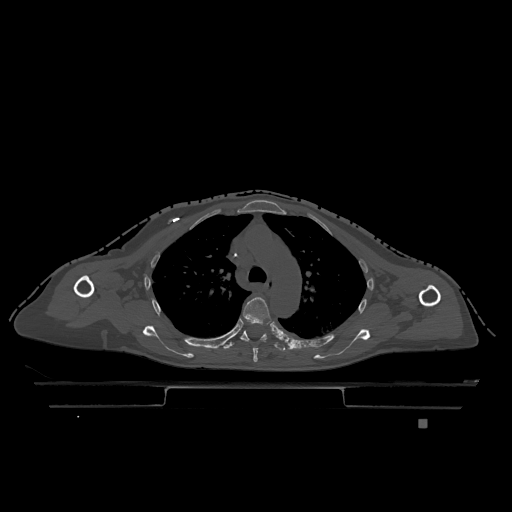
CT including the spine, one axial slice; slice 860 of 1317 in the series (ordered by position); bone window (W 1800 / L 400 HU); 0.5 mm slice thickness; 512 × 512 image matrix, field of view 500 × 500 mm. Female patient, age 74 years. From the clinical record (not read from this slice): primary cancer: lung; vertebrae with lytic lesions (as recorded): T1, T4, T5, T6, L4, L5.
Outlined on this slice (semi-automatic segmentation, software-assisted and operator-edited):
- T4 vertebra: box from (x=240, y=297) to (x=272, y=362) px
- T5 vertebra: (x=221, y=330)–(x=286, y=351)